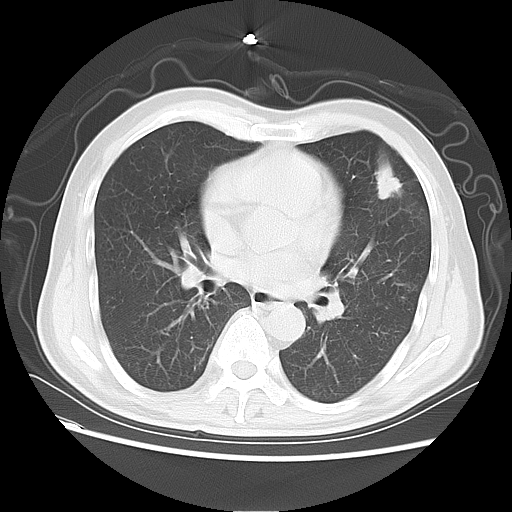
Chest CT, one axial slice; slice 32 of 64 in the series (ordered by position); 120 kVp; lung window (W 1500 / L -600 HU); 5 mm slice thickness; 512 × 512 image matrix, field of view 368 × 368 mm. Patient: male, 60 years. Case-level facts recorded for this patient, not image findings: clinical TNM (as recorded): T2a N0 M0; histopathological grade: G3.
Structures marked on this image (rectangle marked by the reading radiologist):
- lung tumour (recorded histology: adenocarcinoma): box from (x=363, y=147) to (x=402, y=209) px